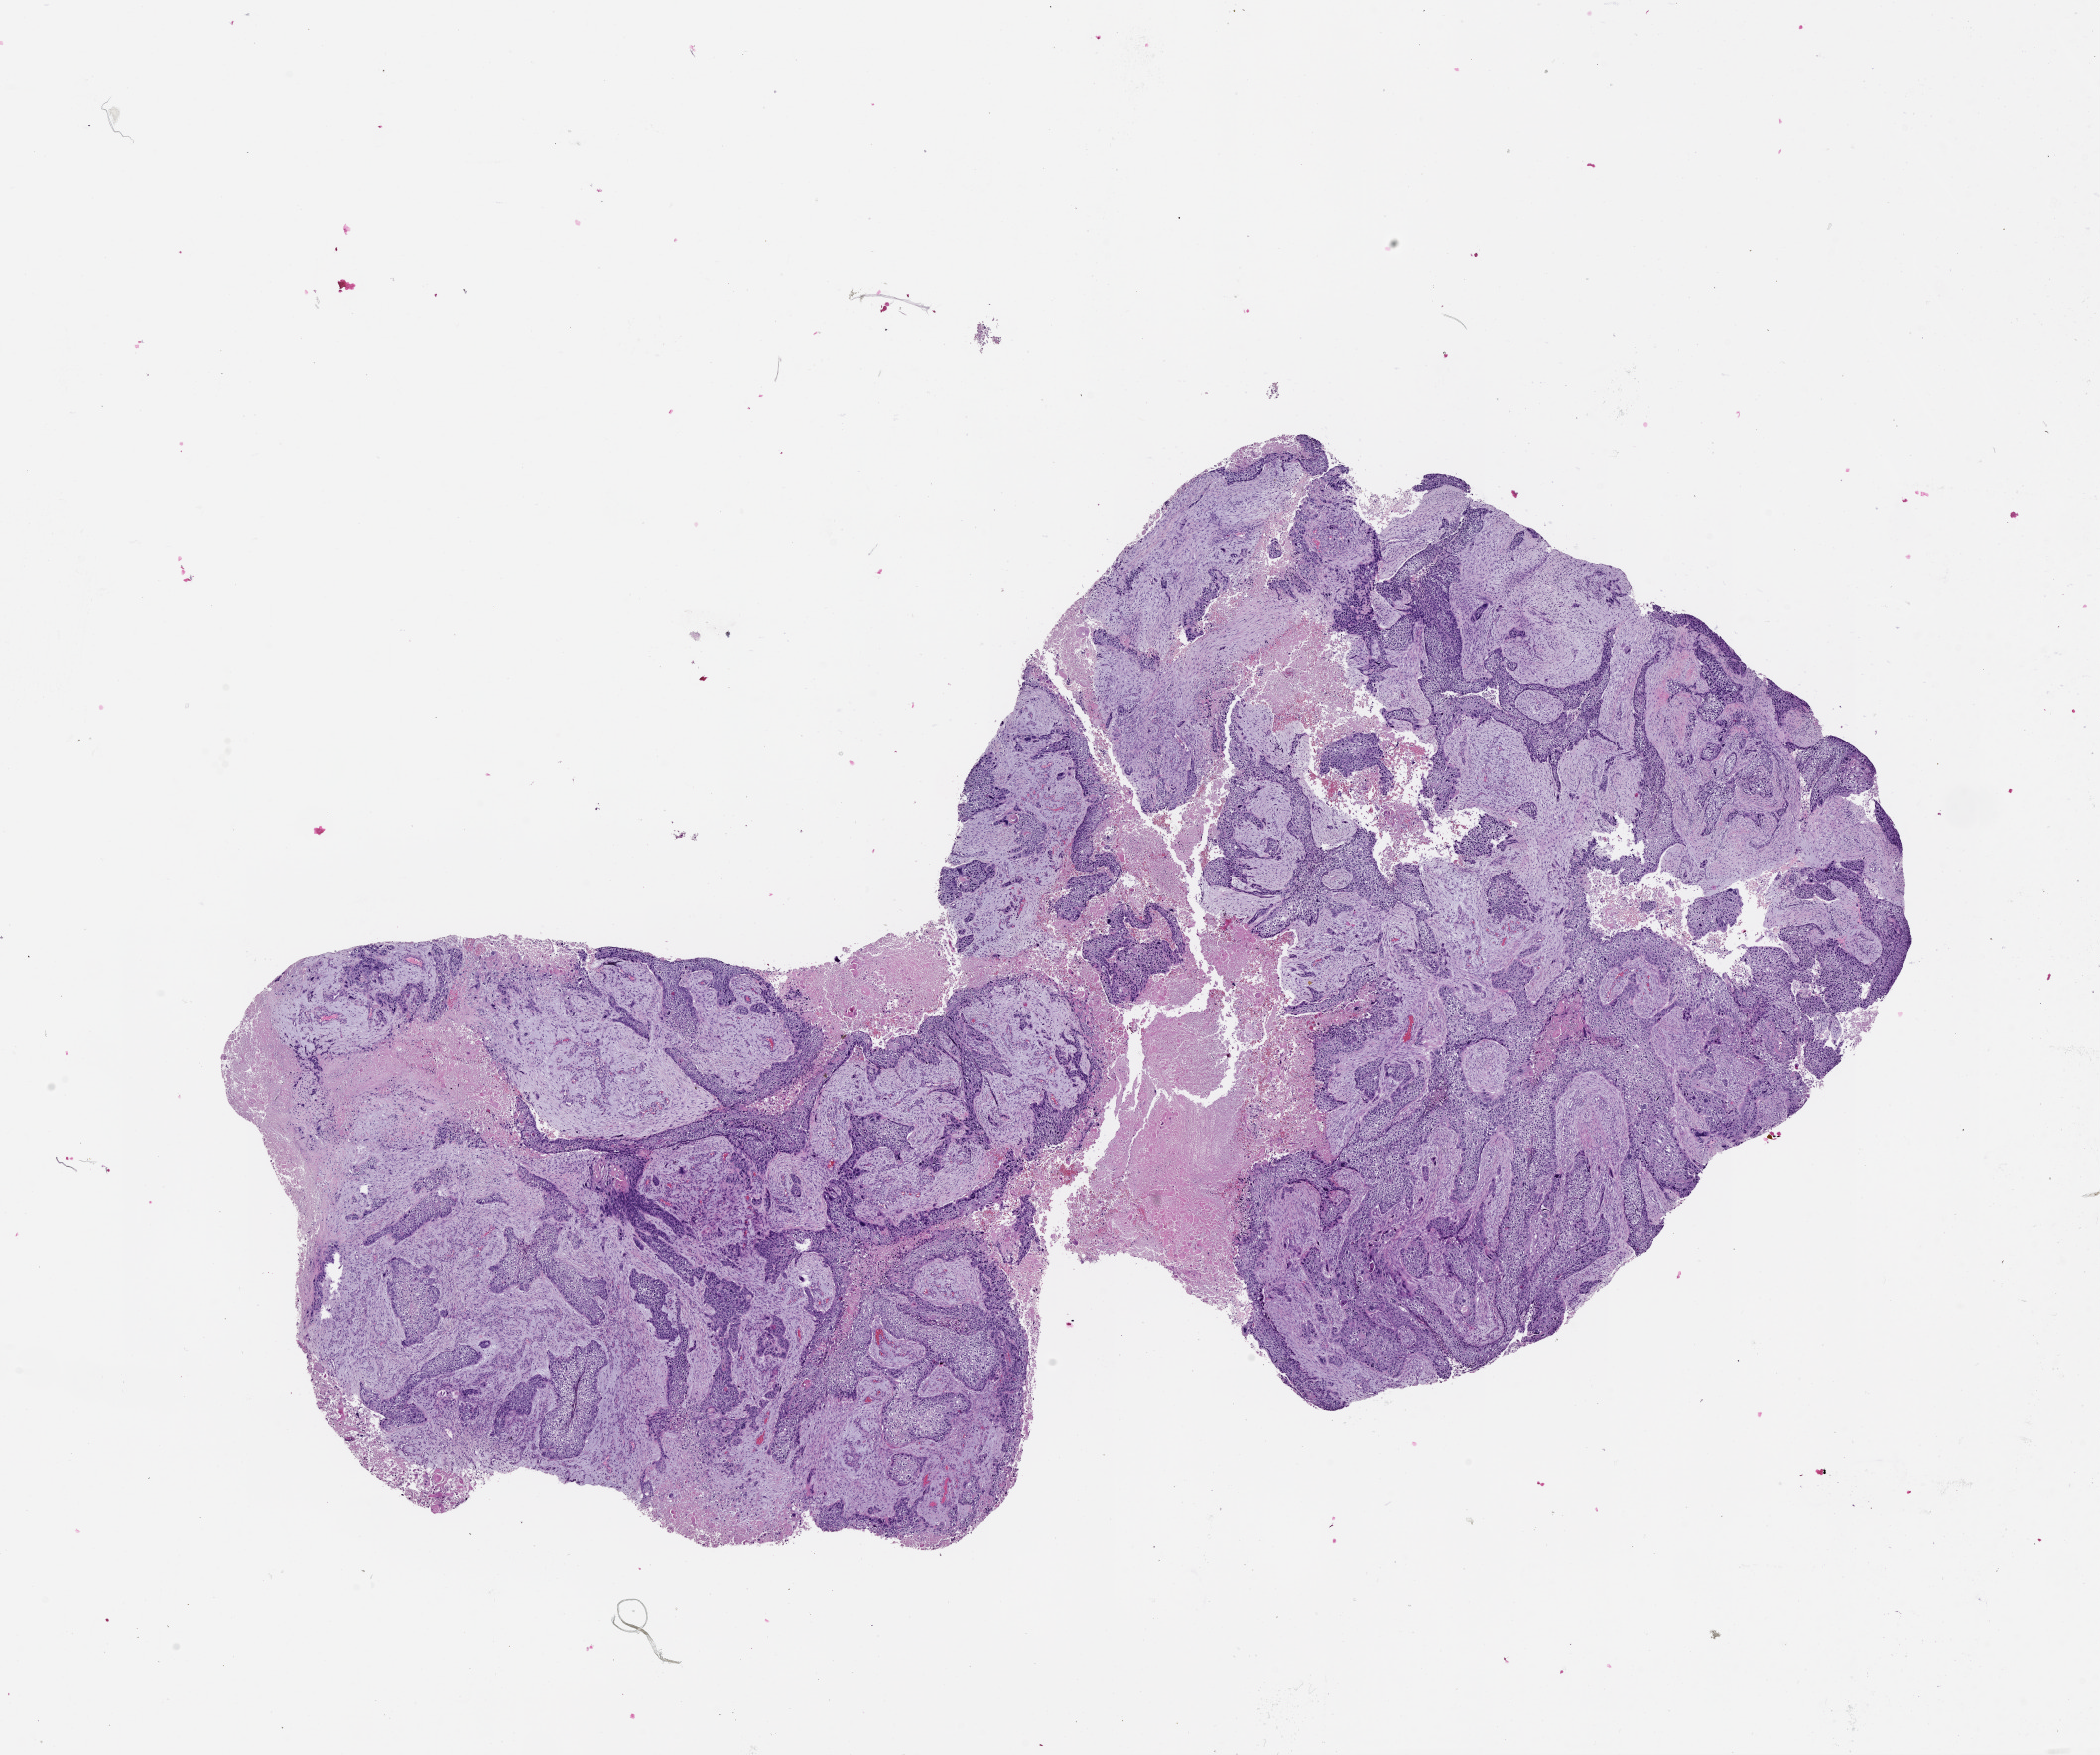
Whole-slide histology image, Hematoxylin and eosin (H&E) stained — a low-resolution overview of the entire scanned area, about 17.0 x 14.2 mm. Tumour tissue sample, lung. 55-year-old male patient.
* patient diagnosis (cohort enrolment): squamous cell carcinoma (lung)